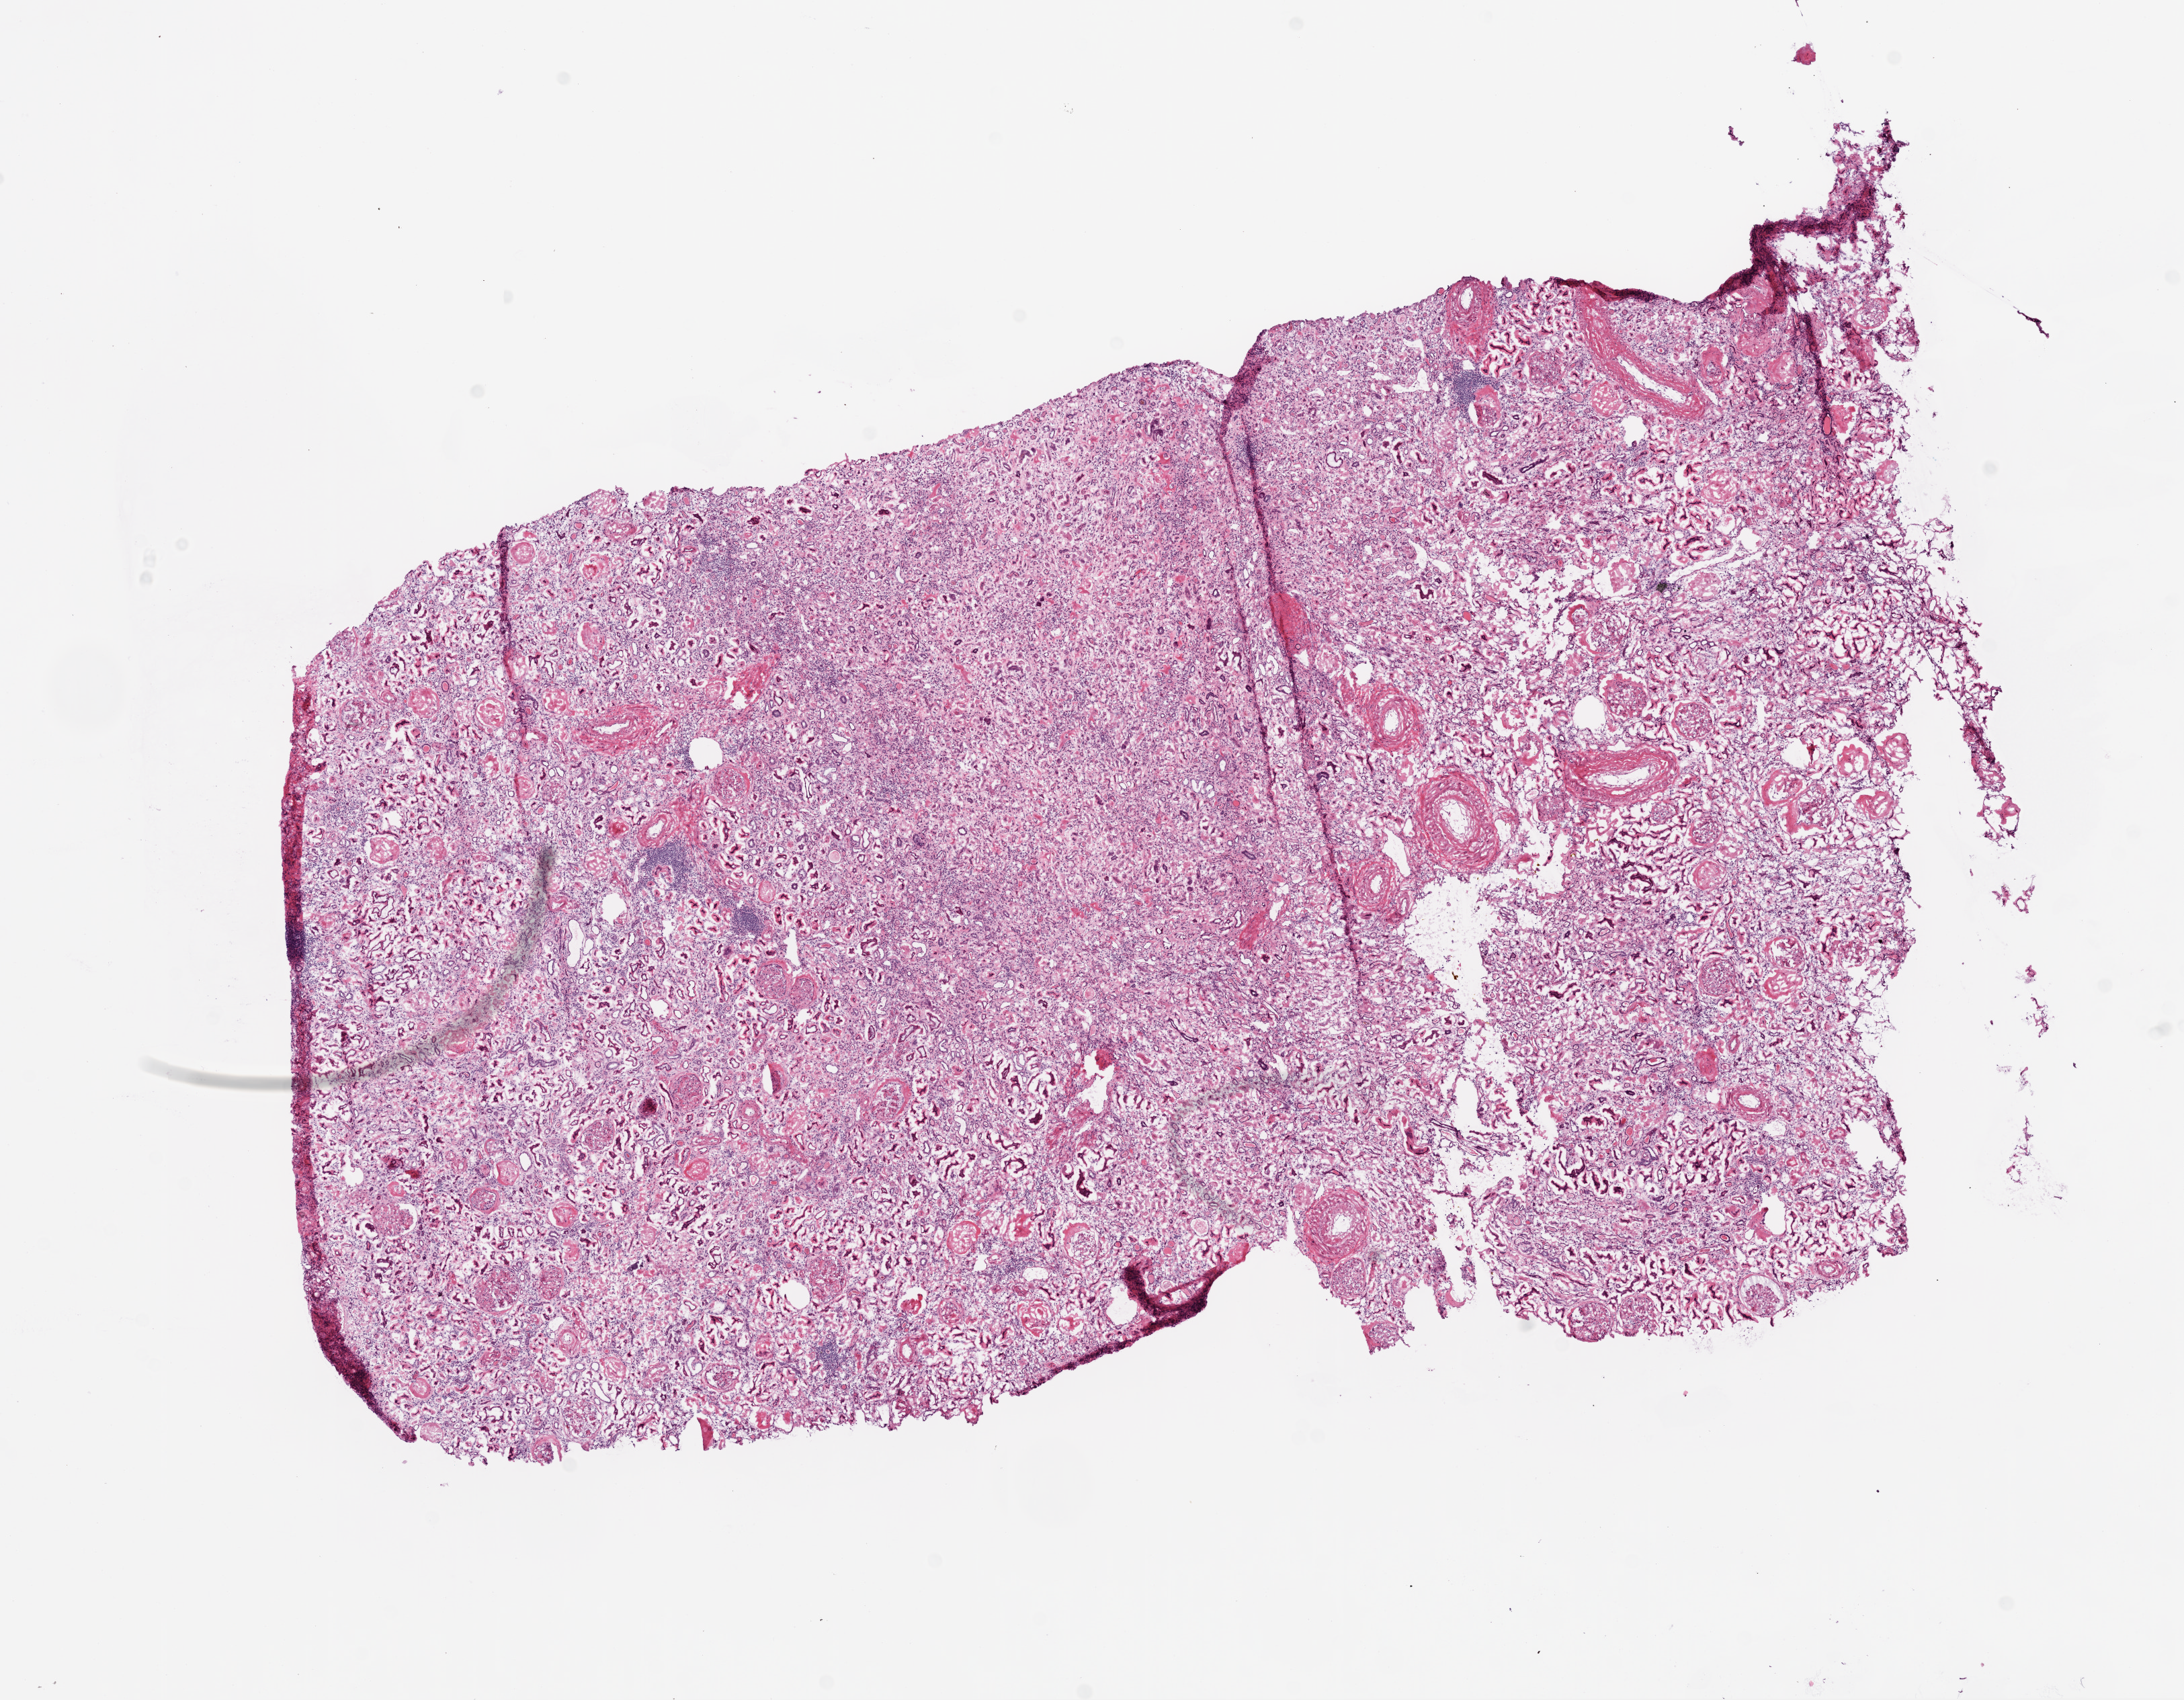
Hematoxylin and eosin (H&E) stained whole-slide image, whole scanned area (about 13.0 x 10.2 mm) shown as a low-resolution overview. Frozen section from the top of the tissue portion. Solid tissue normal (non-tumour tissue) sample from the kidney. Male patient; age at initial diagnosis 51 years.
This section: solid tissue normal sample (biorepository sample class). Patient diagnosis: Clear cell adenocarcinoma, NOS.